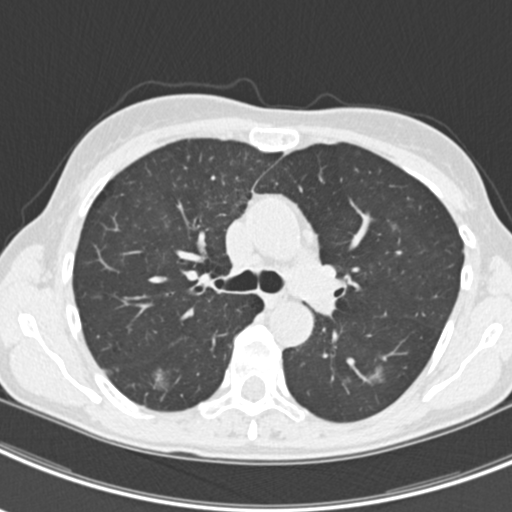
Axial slice from a low-dose chest CT screening exam; second annual screen; lung window (W 1500 / L -600 HU); 2 mm slice thickness; standard (soft-tissue) reconstruction kernel (B30f); slice 70 of 219 in the series; 512 × 512 image matrix. Female, age 63 years at enrolment. Current smoker at enrolment.
2 expert-annotated lung lesions on this slice (largest first), box from (x=365, y=360) to (x=402, y=393) px; (x=144, y=364)–(x=178, y=397). The screening reader recorded 9 non-calcified nodules or masses ≥4 mm on this exam; which of them these boxes mark is not recorded. Official screen result: positive, other. Lung cancer was diagnosed 408 days after this screen (after the third annual screen): bronchiolo-alveolar adenocarcinoma, NOS, right upper lobe, right middle lobe, right lower lobe, left upper lobe, left lower lobe, moderately differentiated (G2), stage IV (AJCC 6th edition).